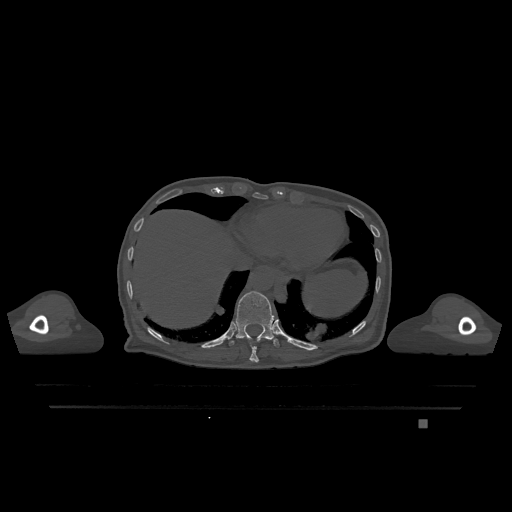
CT including the spine, one axial slice; slice 606 of 1317 in the series (ordered by position); bone window (W 1800 / L 400 HU); 0.5 mm slice thickness; 512 × 512 image matrix, field of view 500 × 500 mm. Female patient, age 74 years. Case-level facts recorded for this patient, not image findings: primary cancer: lung; vertebrae with lytic lesions (as recorded): T1, T4, T5, T6, L4, L5.
Structures marked on this image (semi-automatically segmented with operator editing):
- T10 vertebra: bounding box (x1, y1, x2, y2) in pixels: (249, 345, 259, 363)
- T11 vertebra: (227, 291, 279, 347)